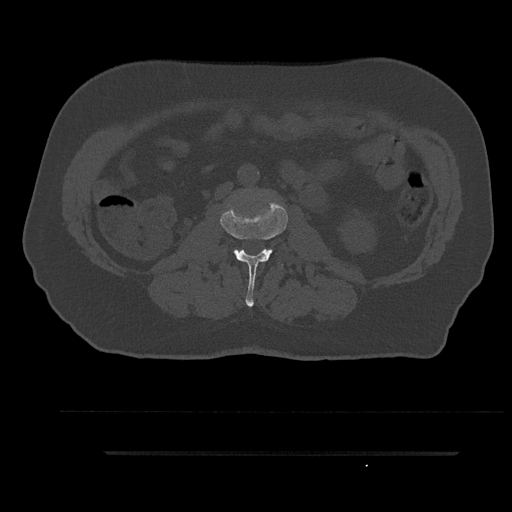
CT including the spine, one axial slice; slice 93 of 797 in the series (ordered by position); reconstruction kernel Br40s/3; 120 kVp; bone window (W 1800 / L 400 HU); 0.5 mm slice thickness; 512 × 512 image matrix. Patient: male, 63 years. Case-level facts recorded for this patient, not image findings: primary cancer: renal.
Structures marked on this image (semi-automatically segmented with operator editing):
- L2 vertebra: bounding box [x1, y1, x2, y2] px = [221, 202, 288, 307]